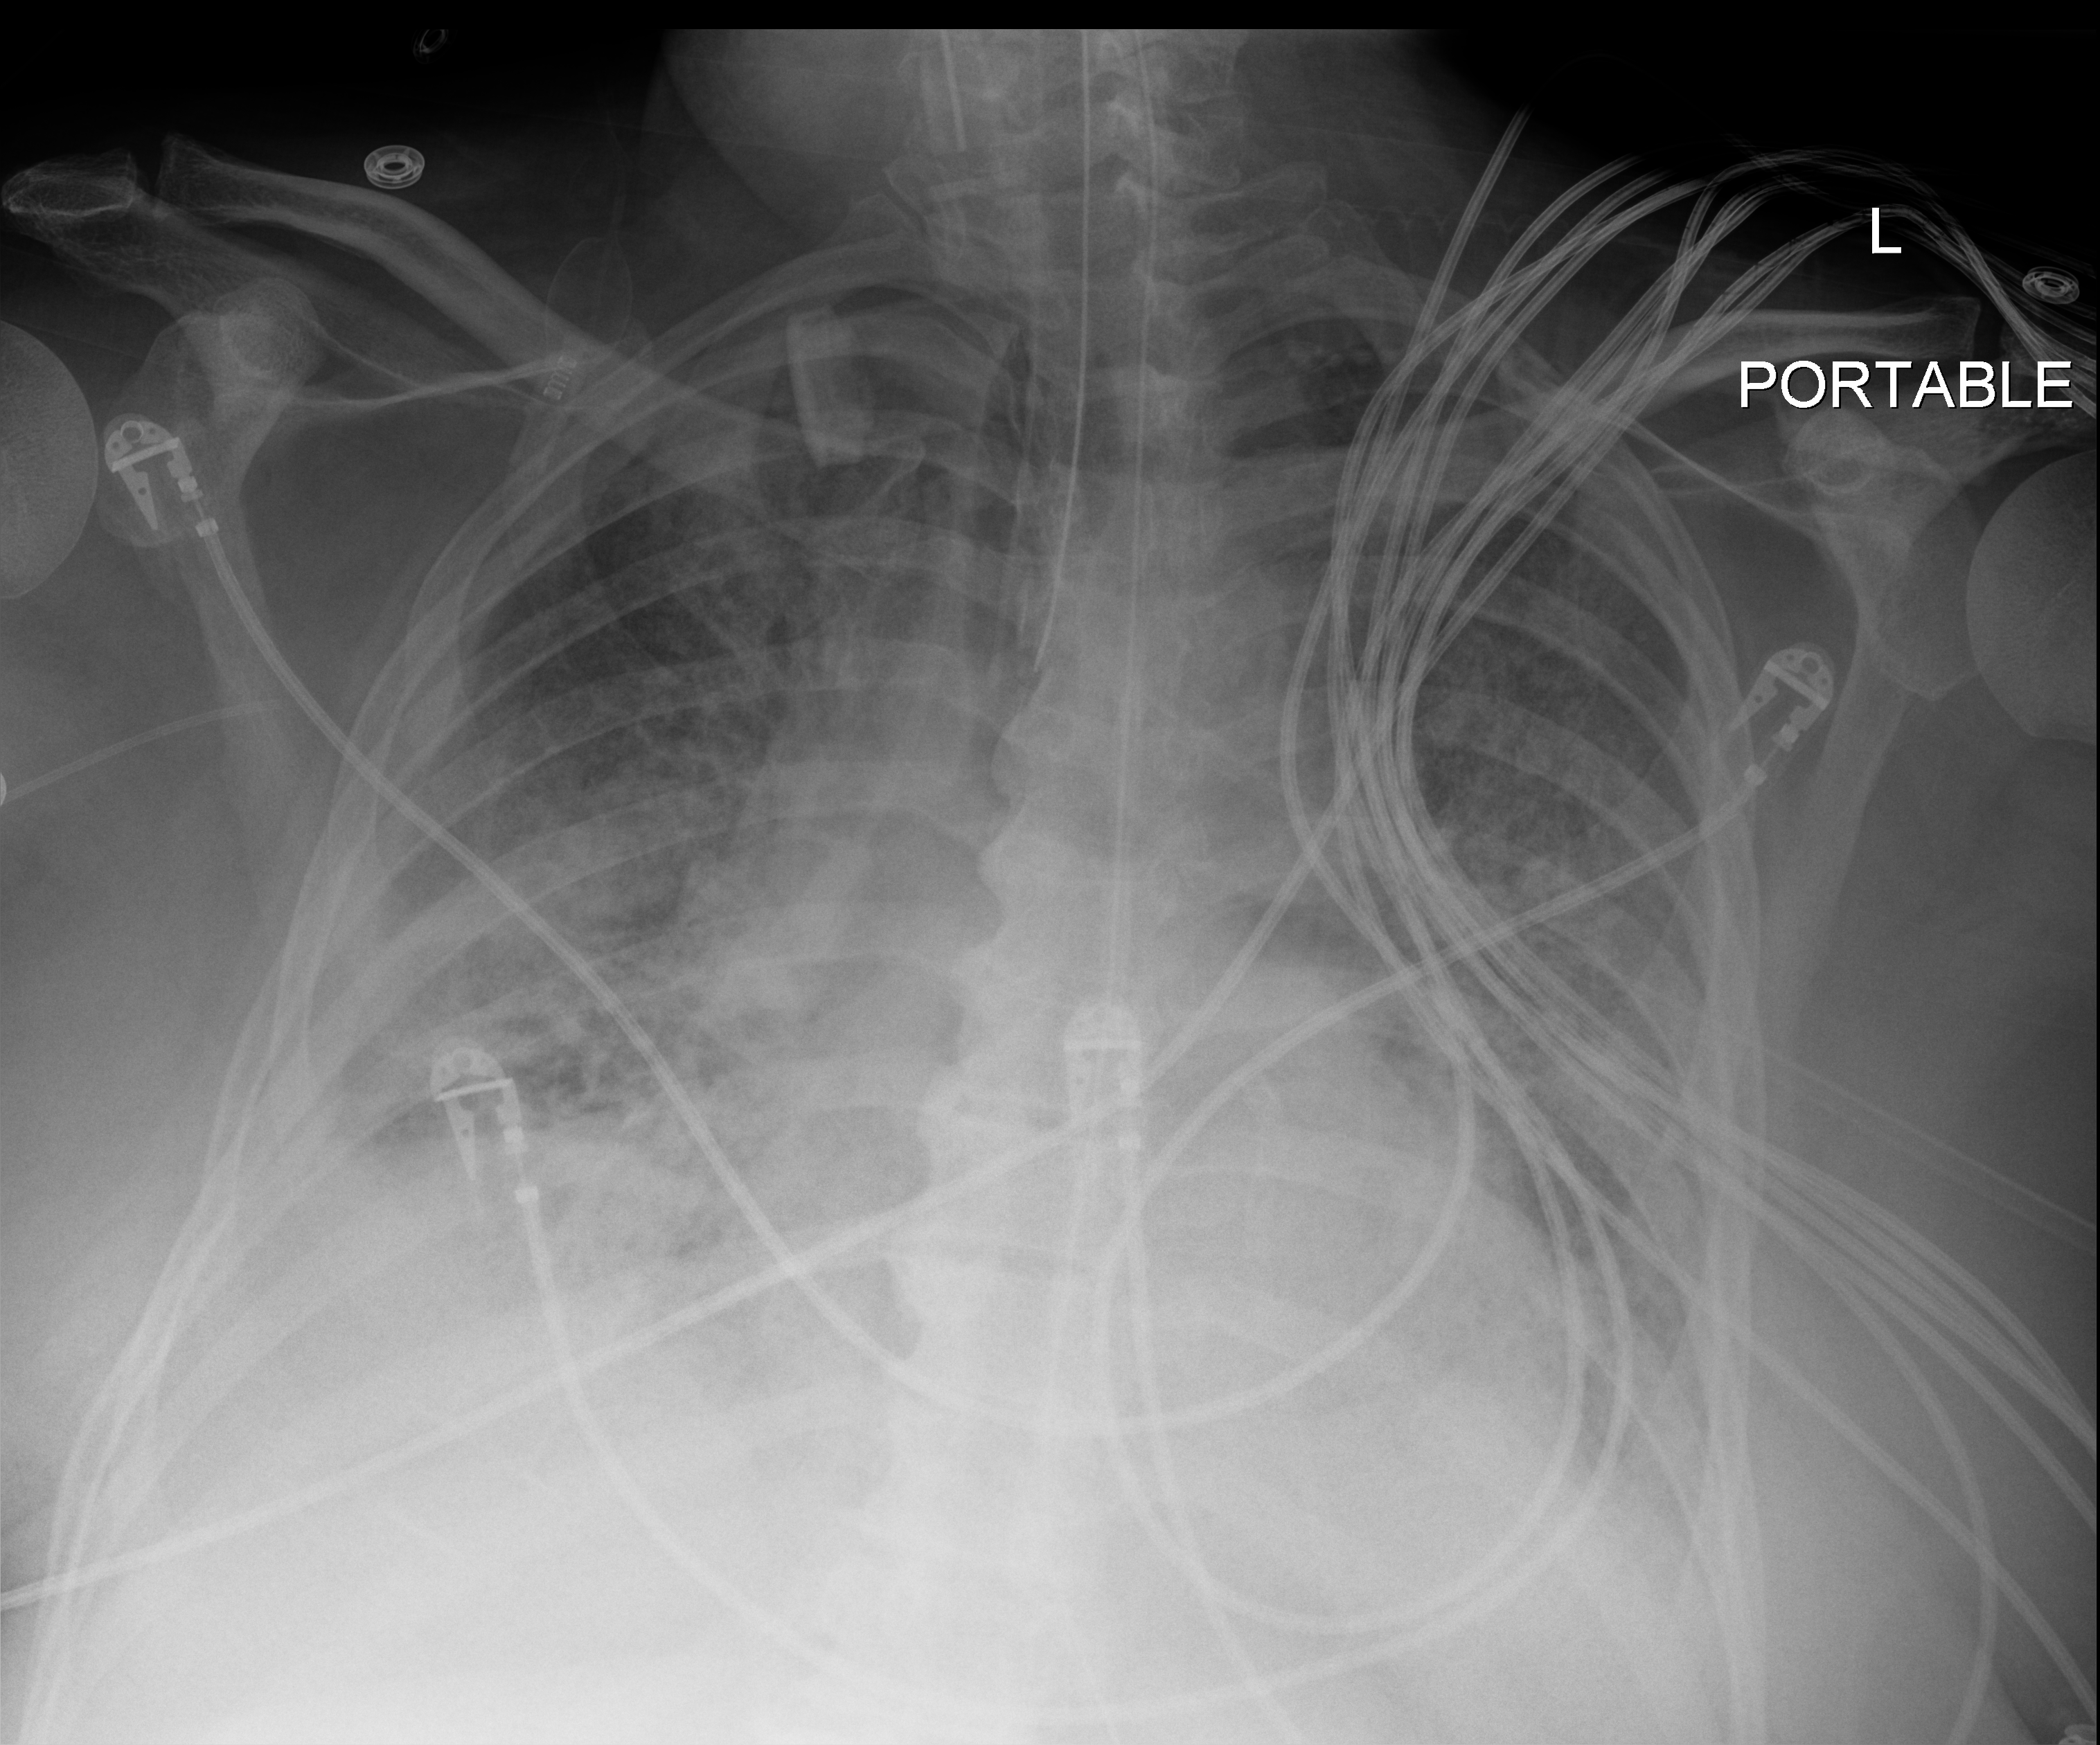
Bedside chest radiograph (digital radiography), anteroposterior (AP) projection. Male patient hospitalised with COVID-19, age 60–74 years.
Hospital-stay facts (about this admission, not read from this image; timing relative to this image not recorded): admitted to intensive care during this hospital stay: yes; mechanically ventilated during this hospital stay: yes; smoking status (admission record): former.